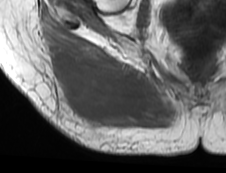
MRI of an extremity soft-tissue mass, one axial slice; slice 29 of 73 in the series (ordered by position); MR volume resampled by the dataset authors to the PET/CT grid (not the native acquisition matrix); 226 × 173 image matrix, field of view 221 × 169 mm. Female patient. Case-level facts recorded for this patient, not image findings: histological type: spindle cell suggestive of myxofibrosarcoma; grade: intermediate; site of the primary tumour: right buttock.
Structures marked on this image (expert contour drawn on MRI and transferred to this co-registered scan by the dataset authors):
- gross tumour volume (mass): bounding box [x1, y1, x2, y2] px = [45, 42, 151, 130]